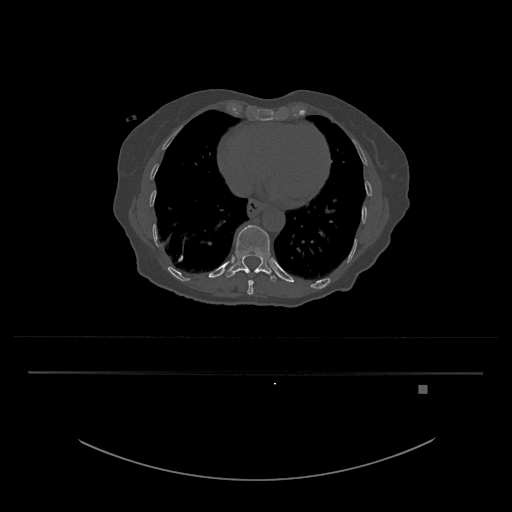
CT including the spine, one axial slice. Position 680 of 797 along the scan axis. 120 kVp. Bone window (W 1800 / L 400 HU). 0.5 mm slice thickness. 512 × 512 image matrix, field of view 500 × 500 mm. Female patient, age 57 years. Case-level facts recorded for this patient, not image findings: primary cancer: cervical.
Annotated regions visible in this slice (semi-automatic segmentation, software-assisted and operator-edited):
- T10 vertebra: bounding box <247,272,254,295> (left, top, right, bottom; pixels)
- T11 vertebra: <225,225,277,282>